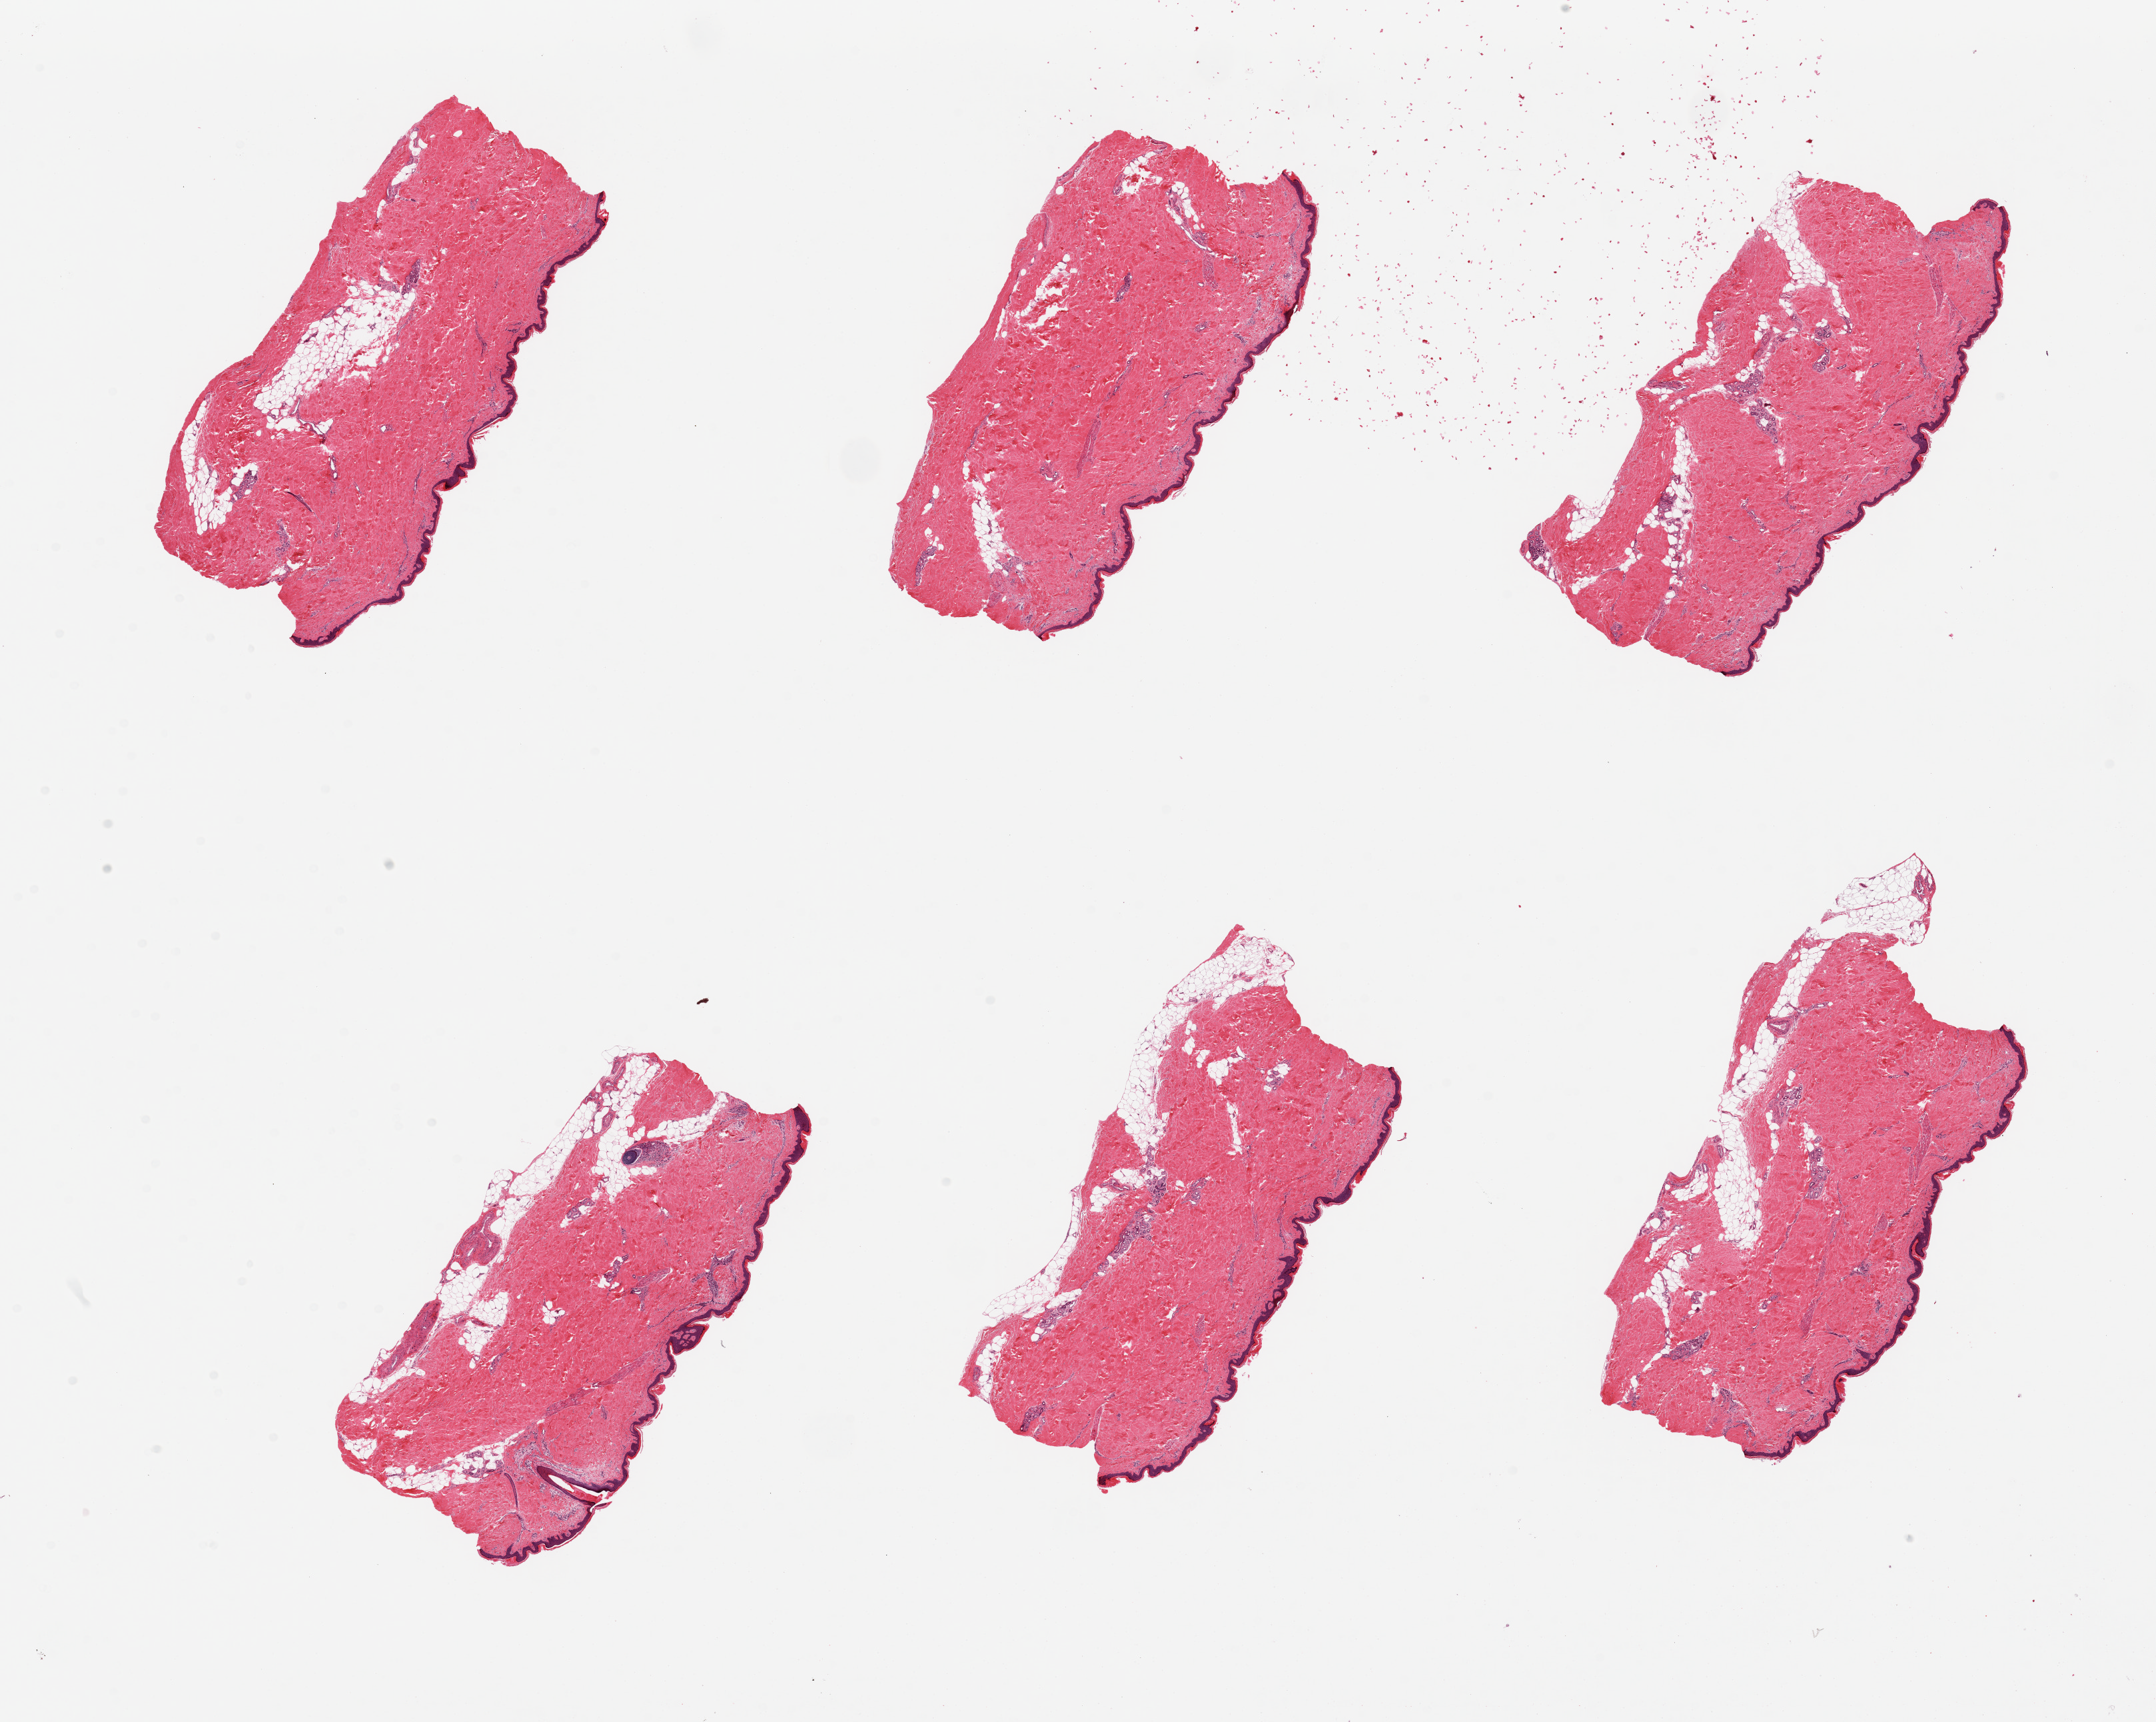
Digitized hematoxylin and eosin (H&E)-stained section, a low-resolution overview of the entire scanned area, about 25.6 x 20.4 mm, PAXgene-fixed paraffin-embedded (PFPE) section, section of skin of lower leg (target tissue), donor tissue sample. Donor sex: male.
Review note (as recorded): 6 pieces. Well trimmed.